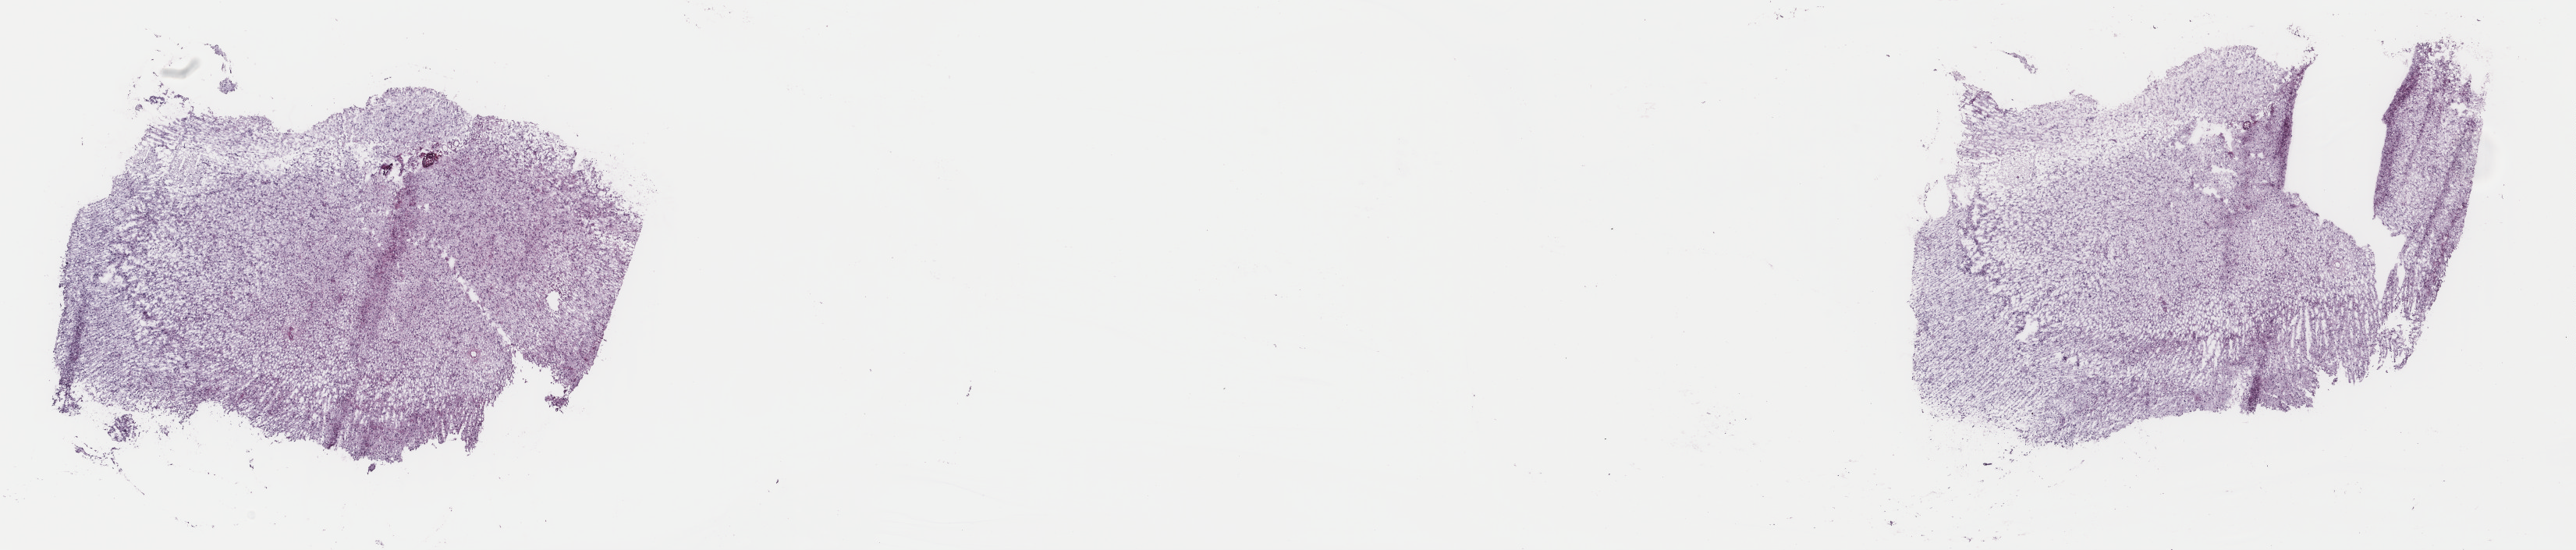
H&E-stained whole-slide image, low-resolution overview of the scanned area, about 26.2 x 5.6 mm (slide scanned at 40x); frozen section from the top of the tissue portion; sample: primary tumour, brain. Patient: male, age at initial diagnosis 22 years. Histologic grade: G3 (poorly differentiated). Slide review estimates, as recorded: tumour cells 75%, tumour nuclei 90%, normal cells 5%, stromal cells 20%, necrosis 0%. Infiltration values recorded for this section: lymphocyte infiltration 0%, monocyte infiltration 0%, neutrophil infiltration 0%.
- diagnosis: Astrocytoma, anaplastic (cerebrum)